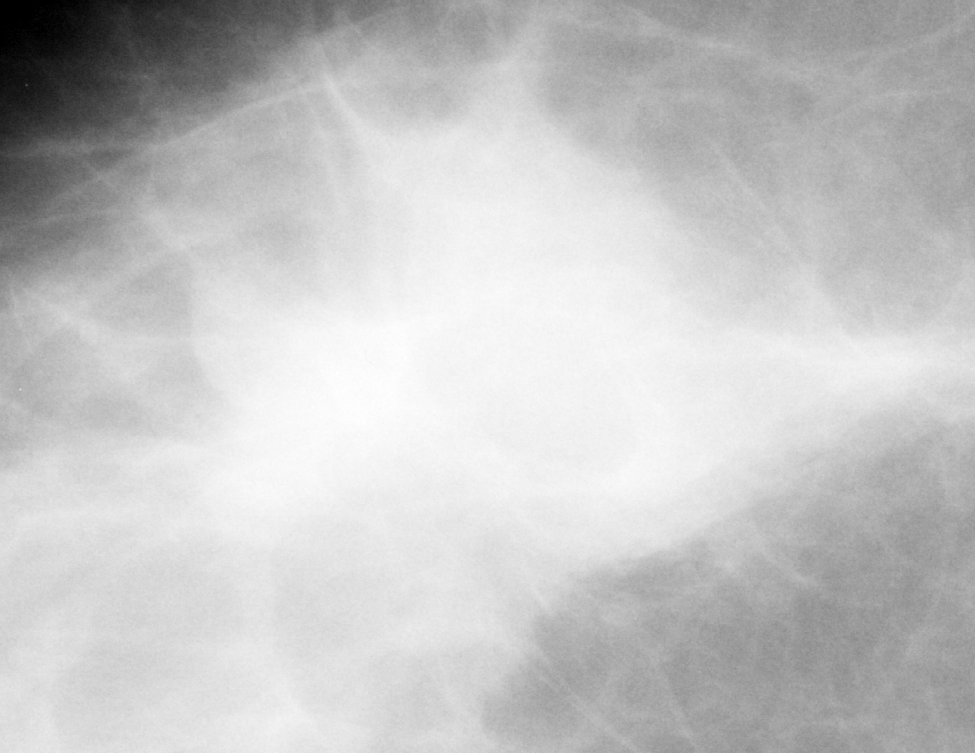
Crop from a digitized film mammogram around one marked abnormality; right breast; CC view; BI-RADS breast density category 3 (scale 1–4).
Mass, shape irregular / architectural distortion, margins obscured / ill defined / spiculated; BI-RADS assessment category 4; pathology (as recorded): malignant.